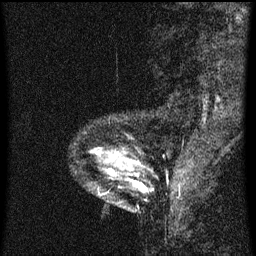
Breast MRI (dynamic contrast-enhanced), one sagittal slice; position 12 of 60 along the scan axis; dynamic contrast-enhanced series, image 2 of 3 at this slice position (ordered by acquisition); 1.5 T; TE 4.2 ms, TR 8 ms; 2 mm slice thickness; 256 × 256 image matrix, field of view 180 × 180 mm. Patient: female, 33 years.
Structures marked on this image (semi-automatically segmented with operator editing):
- analysis volume of interest (the breast-tissue region the enhancement analysis was run in; not a lesion): bounding box (x1, y1, x2, y2) in pixels: (100, 152, 146, 189)
- tumour enhancement mask (voxels above the 70 % enhancement threshold inside the analysis volume of interest): (136, 182, 140, 185)